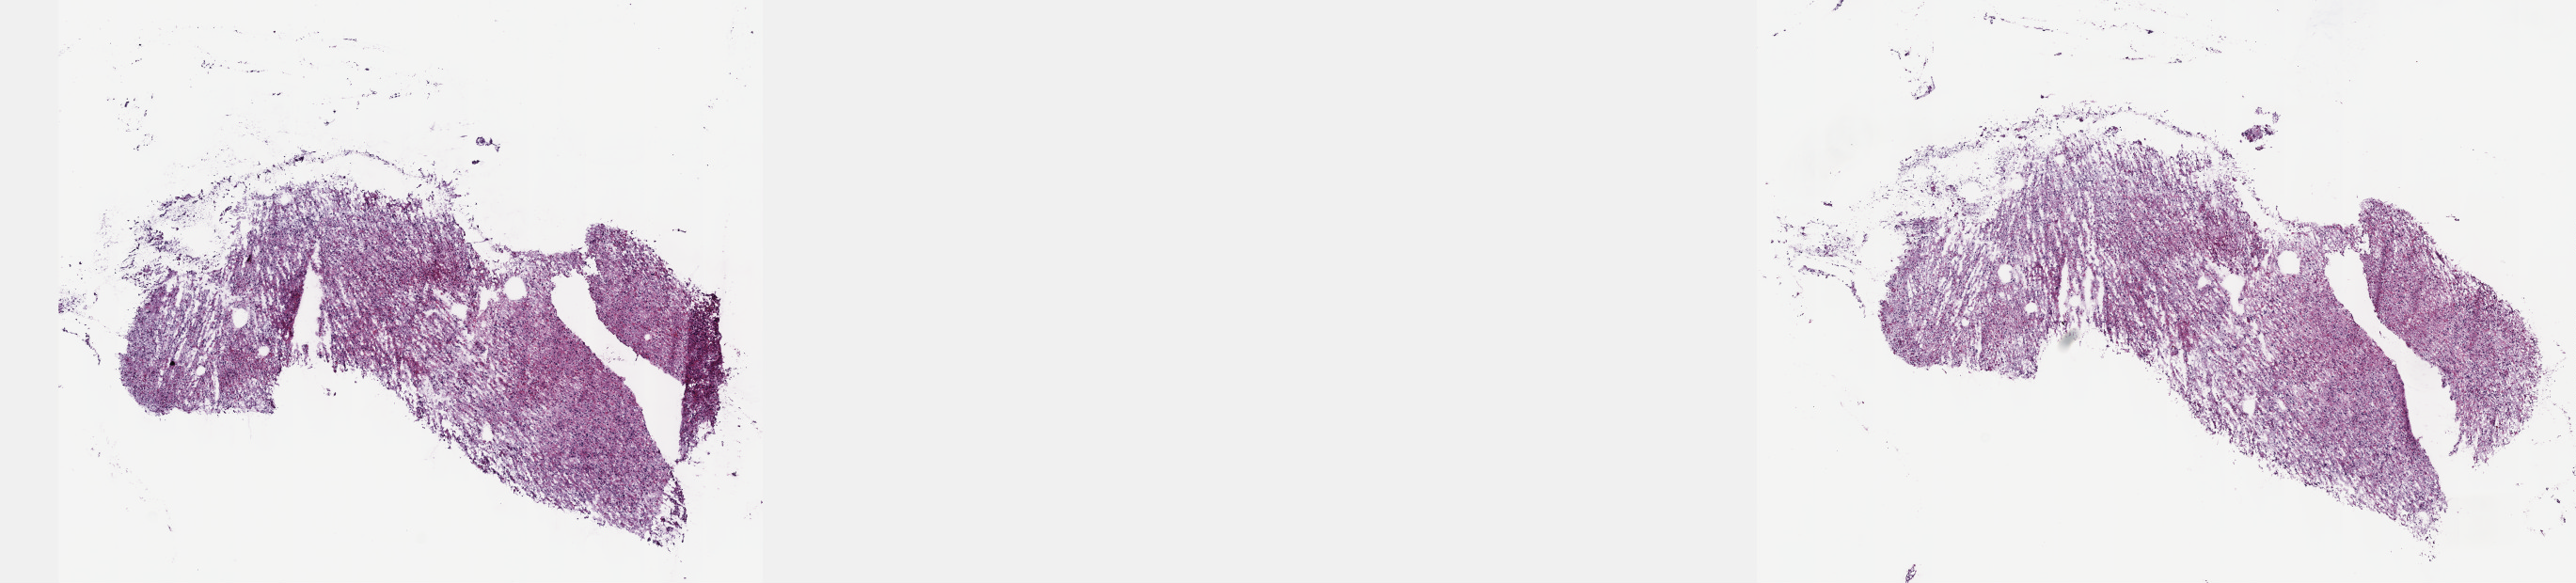
Whole-slide histology image, H&E-stained — shown as a low-resolution overview of the whole scanned area (about 22.1 x 5.0 mm, acquisition: 40x scan); frozen section from the top of the tissue portion; brain, primary tumour sample. Patient: male, age at initial diagnosis 31 years. Histologic grade: G2 (moderately differentiated). Pathologist review of this section (percent, as recorded): tumour cells 60%, tumour nuclei 90%, normal cells 10%, stromal cells 30%, necrosis 0%. Inflammatory infiltration, as recorded: lymphocyte infiltration 0%, monocyte infiltration 0%, neutrophil infiltration 0%.
Diagnosis: Astrocytoma, NOS (cerebrum). Laterality: left.